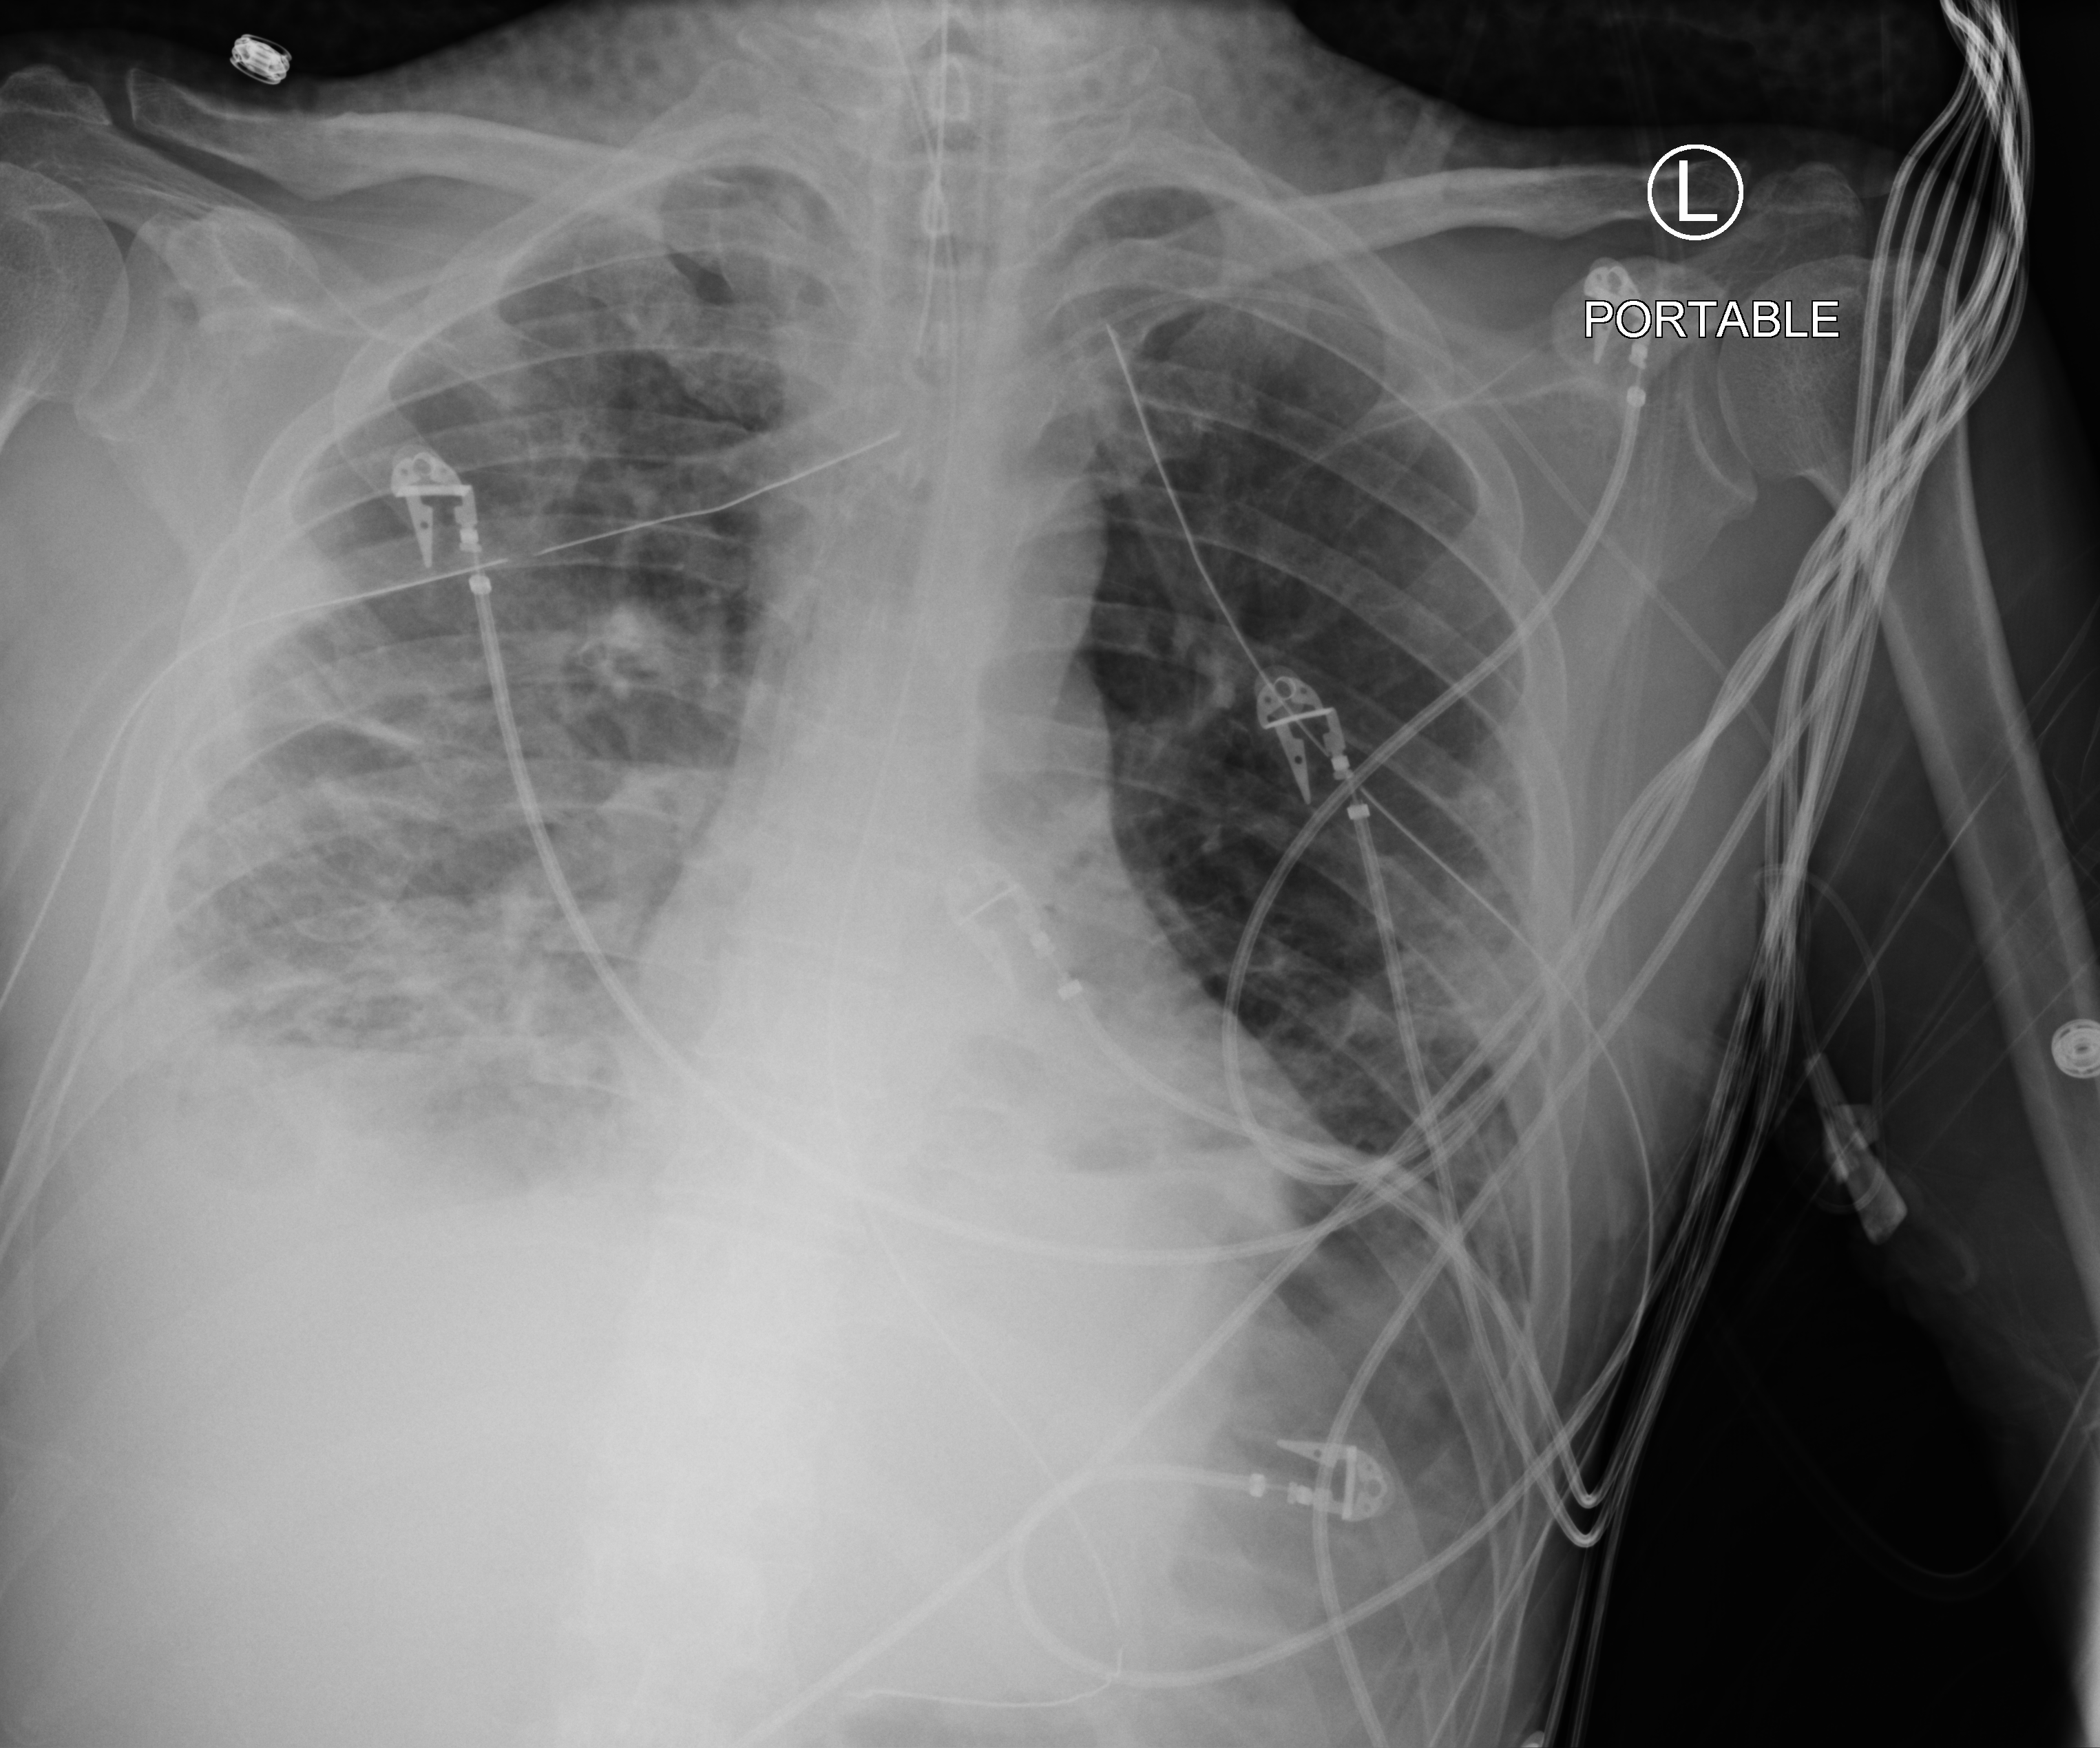
Bedside chest radiograph (computed radiography), anteroposterior (AP) projection. Male patient hospitalised with COVID-19, age 18–59 years.
Admission-level facts for this patient (not findings on this image; timing relative to this image not recorded):
- length of hospital stay: 96 days